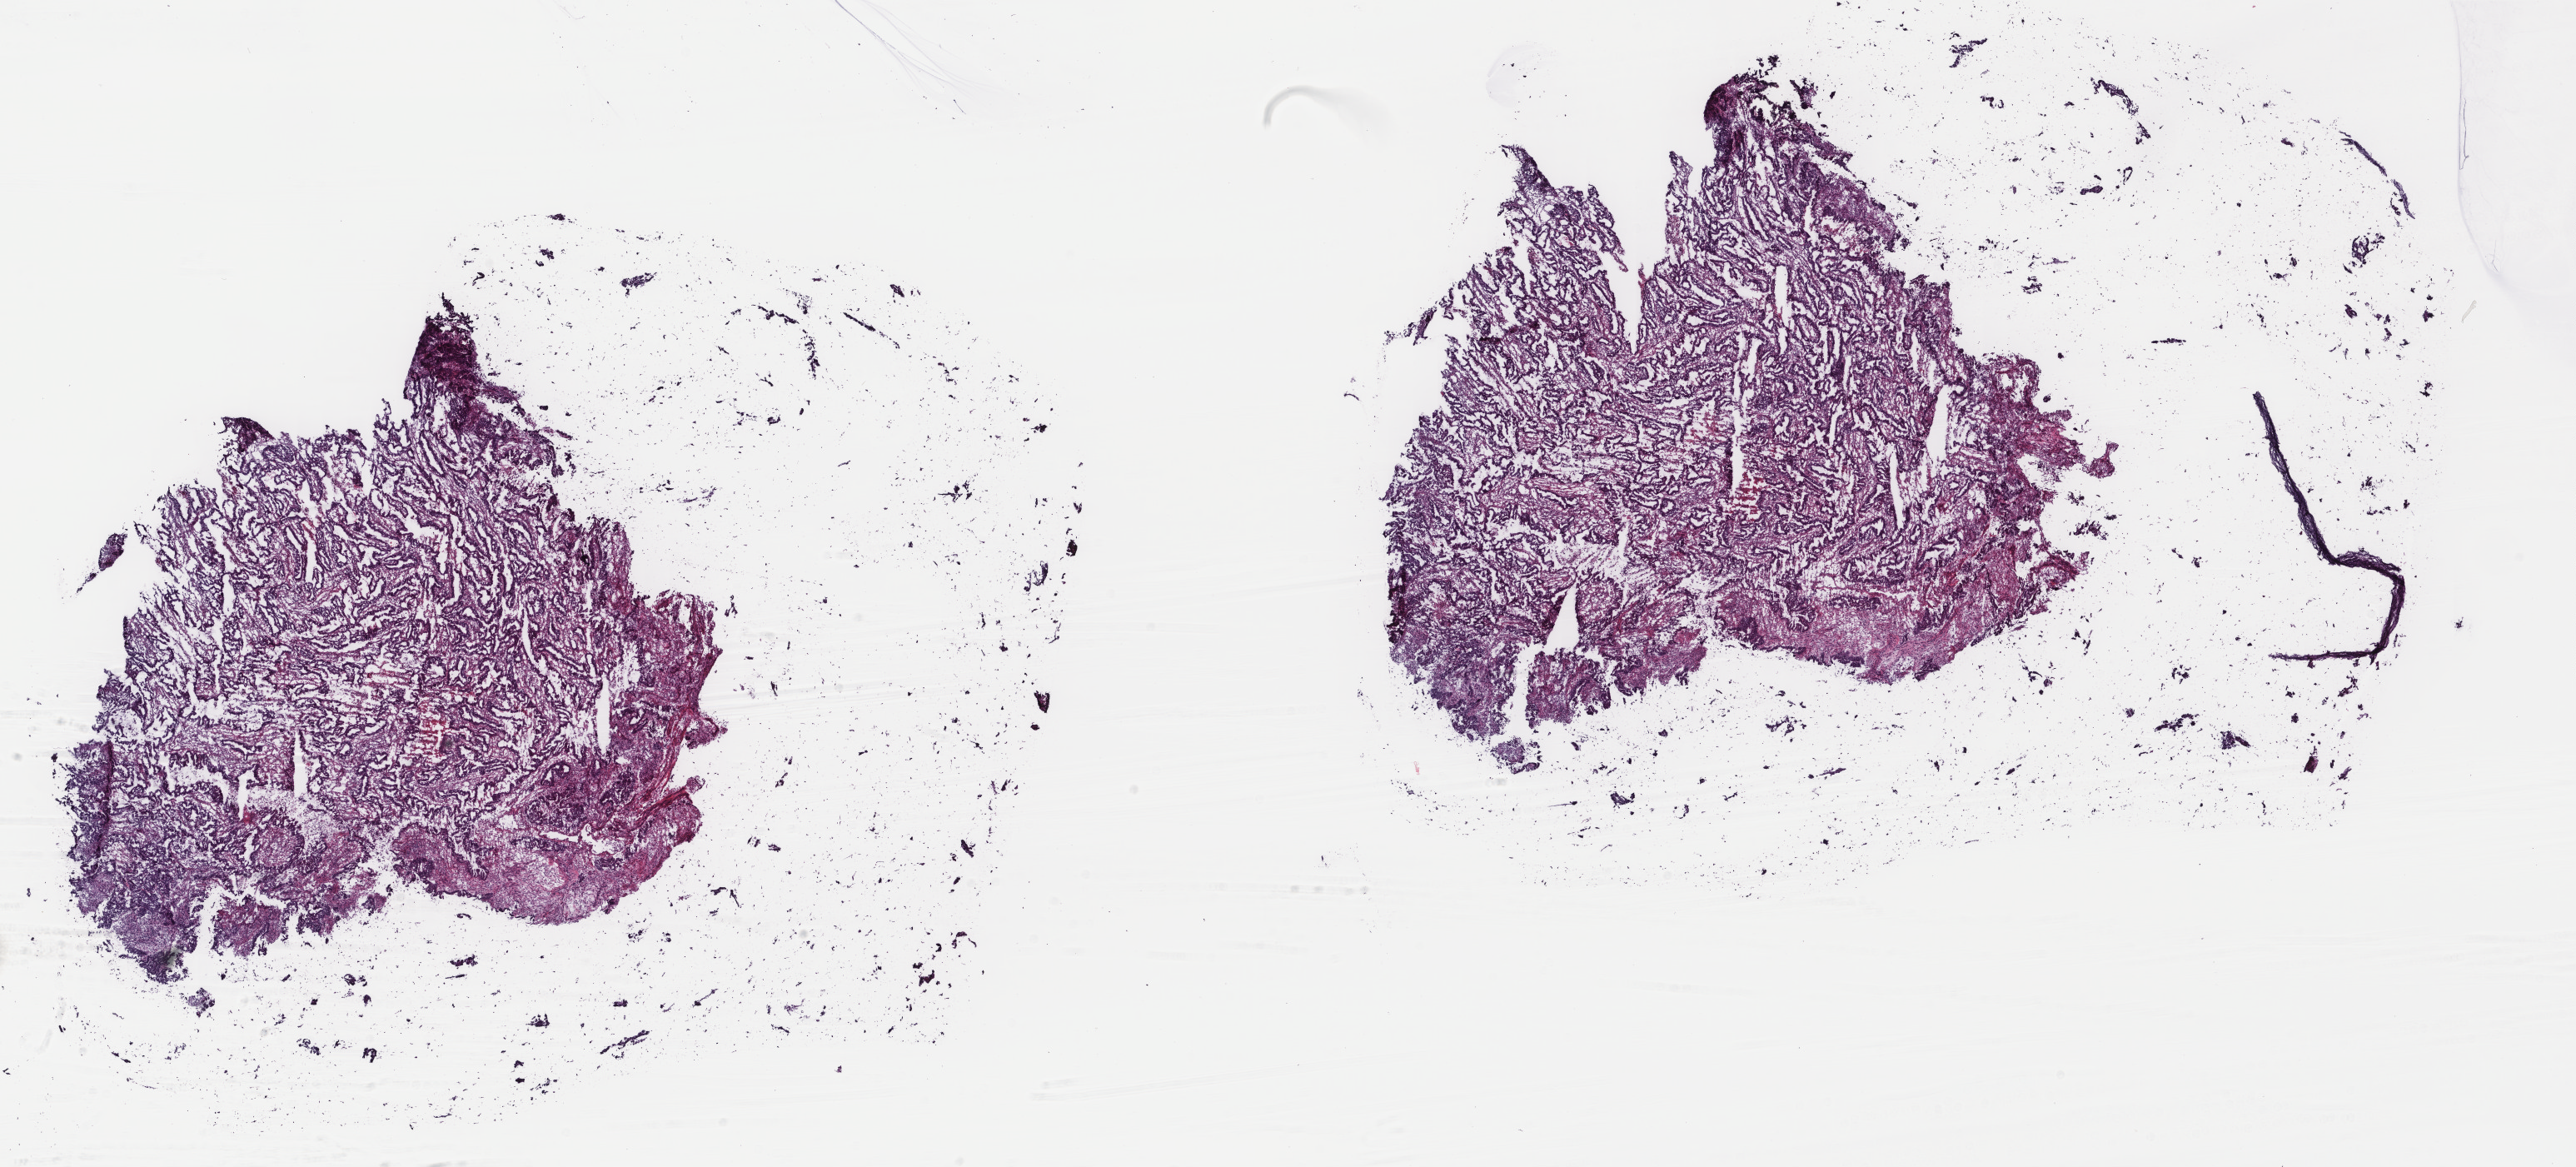
Whole-slide histology image, H&E — low-resolution overview of the scanned area, about 24.6 x 11.1 mm. Frozen section. Sample: primary tumour, uterus. Female patient; age at initial diagnosis 60 years. Histologic grade: G1 (well differentiated). Composition of this section per pathologist review: tumour cells 40%, tumour nuclei 60%, normal cells 20%, stromal cells 20%, necrosis 20%. Infiltration values recorded for this section: lymphocyte infiltration 20%, monocyte infiltration 20%, neutrophil infiltration 20%.
FIGO stage: IA. Diagnosis: Endometrioid adenocarcinoma, NOS (endometrium).